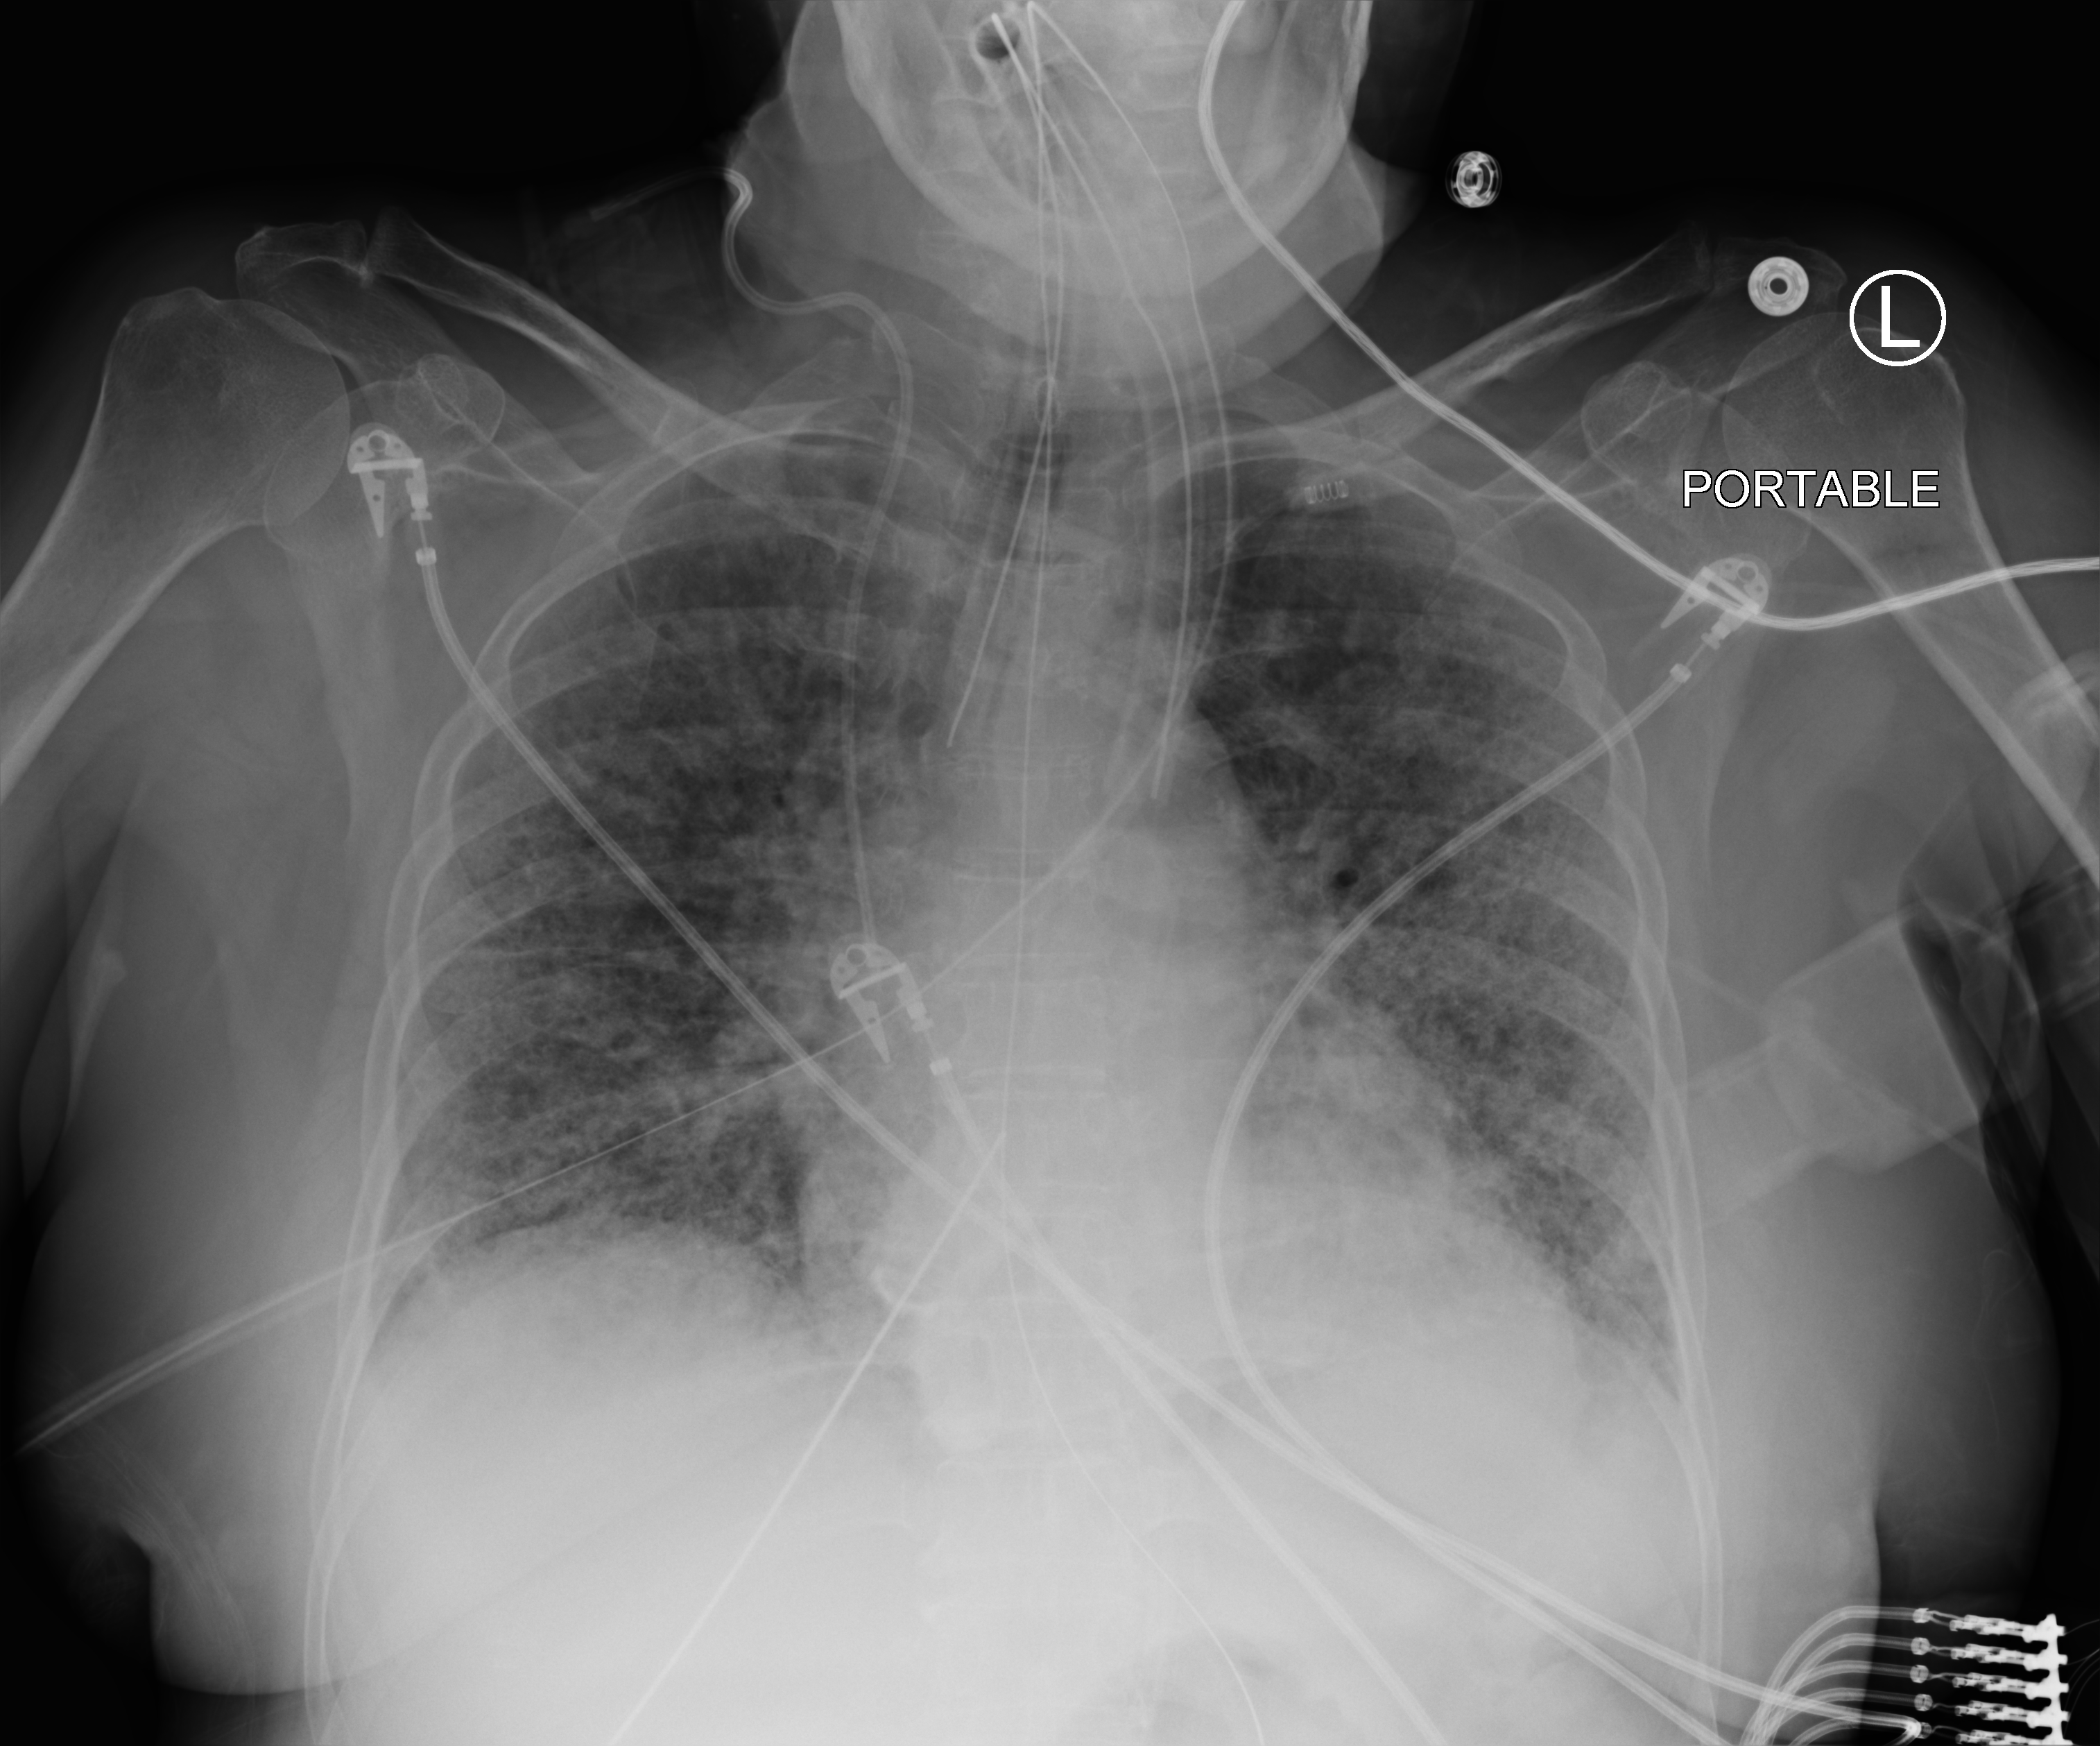
Portable chest radiograph; anteroposterior (AP) projection. Patient hospitalised with COVID-19; female, aged 60–74 years.
From the hospital-stay record, not from the radiograph (when in the stay this image was taken is not recorded):
- admitted to intensive care during this hospital stay: yes
- length of hospital stay: 14 days